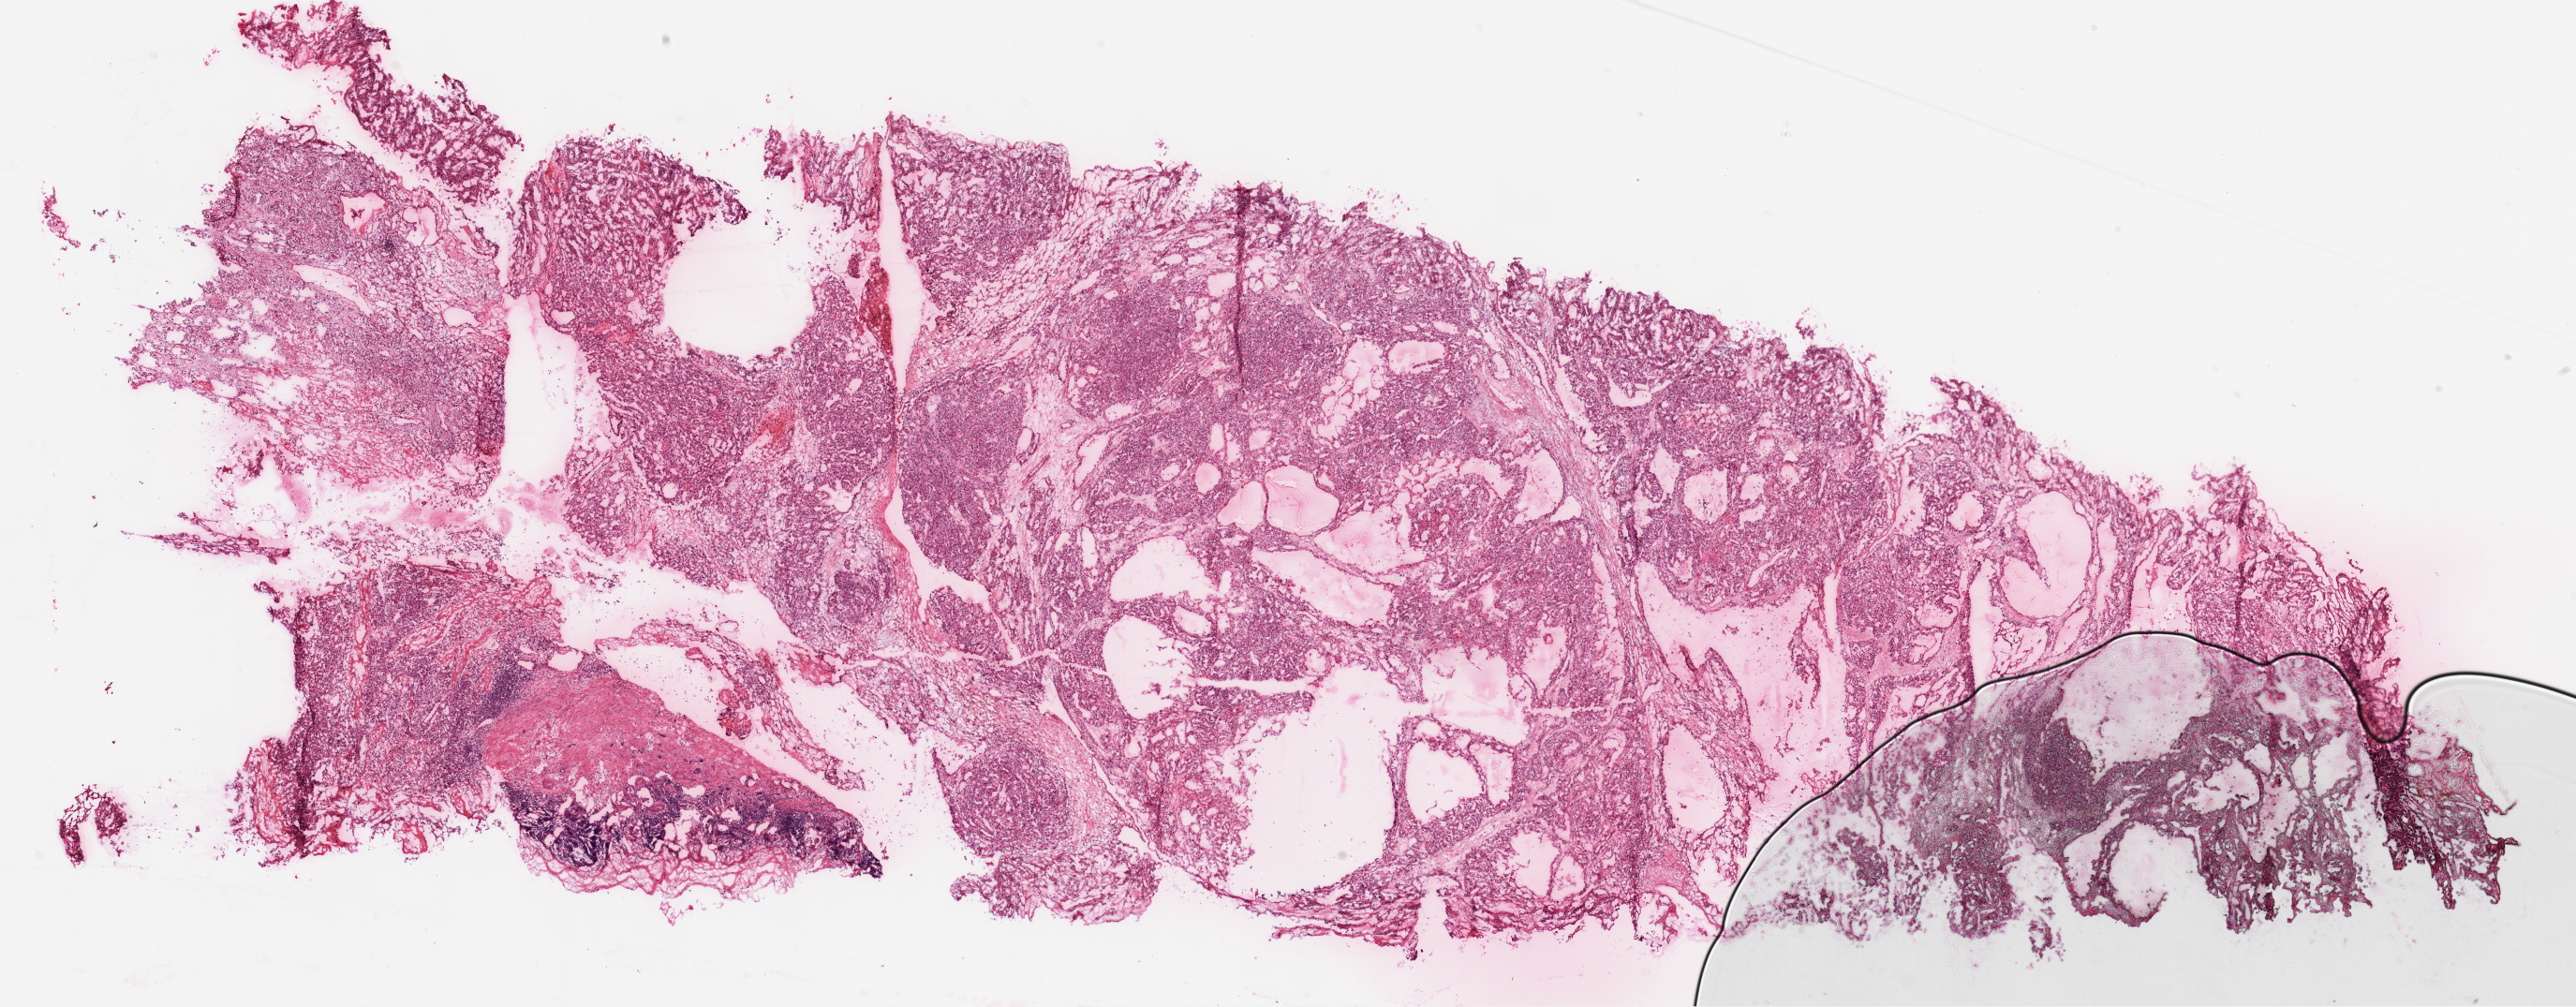
Whole-slide histology image, Hematoxylin and eosin (H&E) stained — a low-resolution overview of the entire scanned area, about 22.1 x 8.6 mm; frozen section from the top of the tissue portion; sample: primary tumour, kidney. Male, age 50 years at initial diagnosis. Histologic grade: G3 (poorly differentiated). Slide review estimates, as recorded: tumour cells 85%, tumour nuclei 75%, normal cells 0%, stromal cells 15%, necrosis 0%.
Diagnosis: Clear cell adenocarcinoma, NOS. AJCC pathologic stage: I.